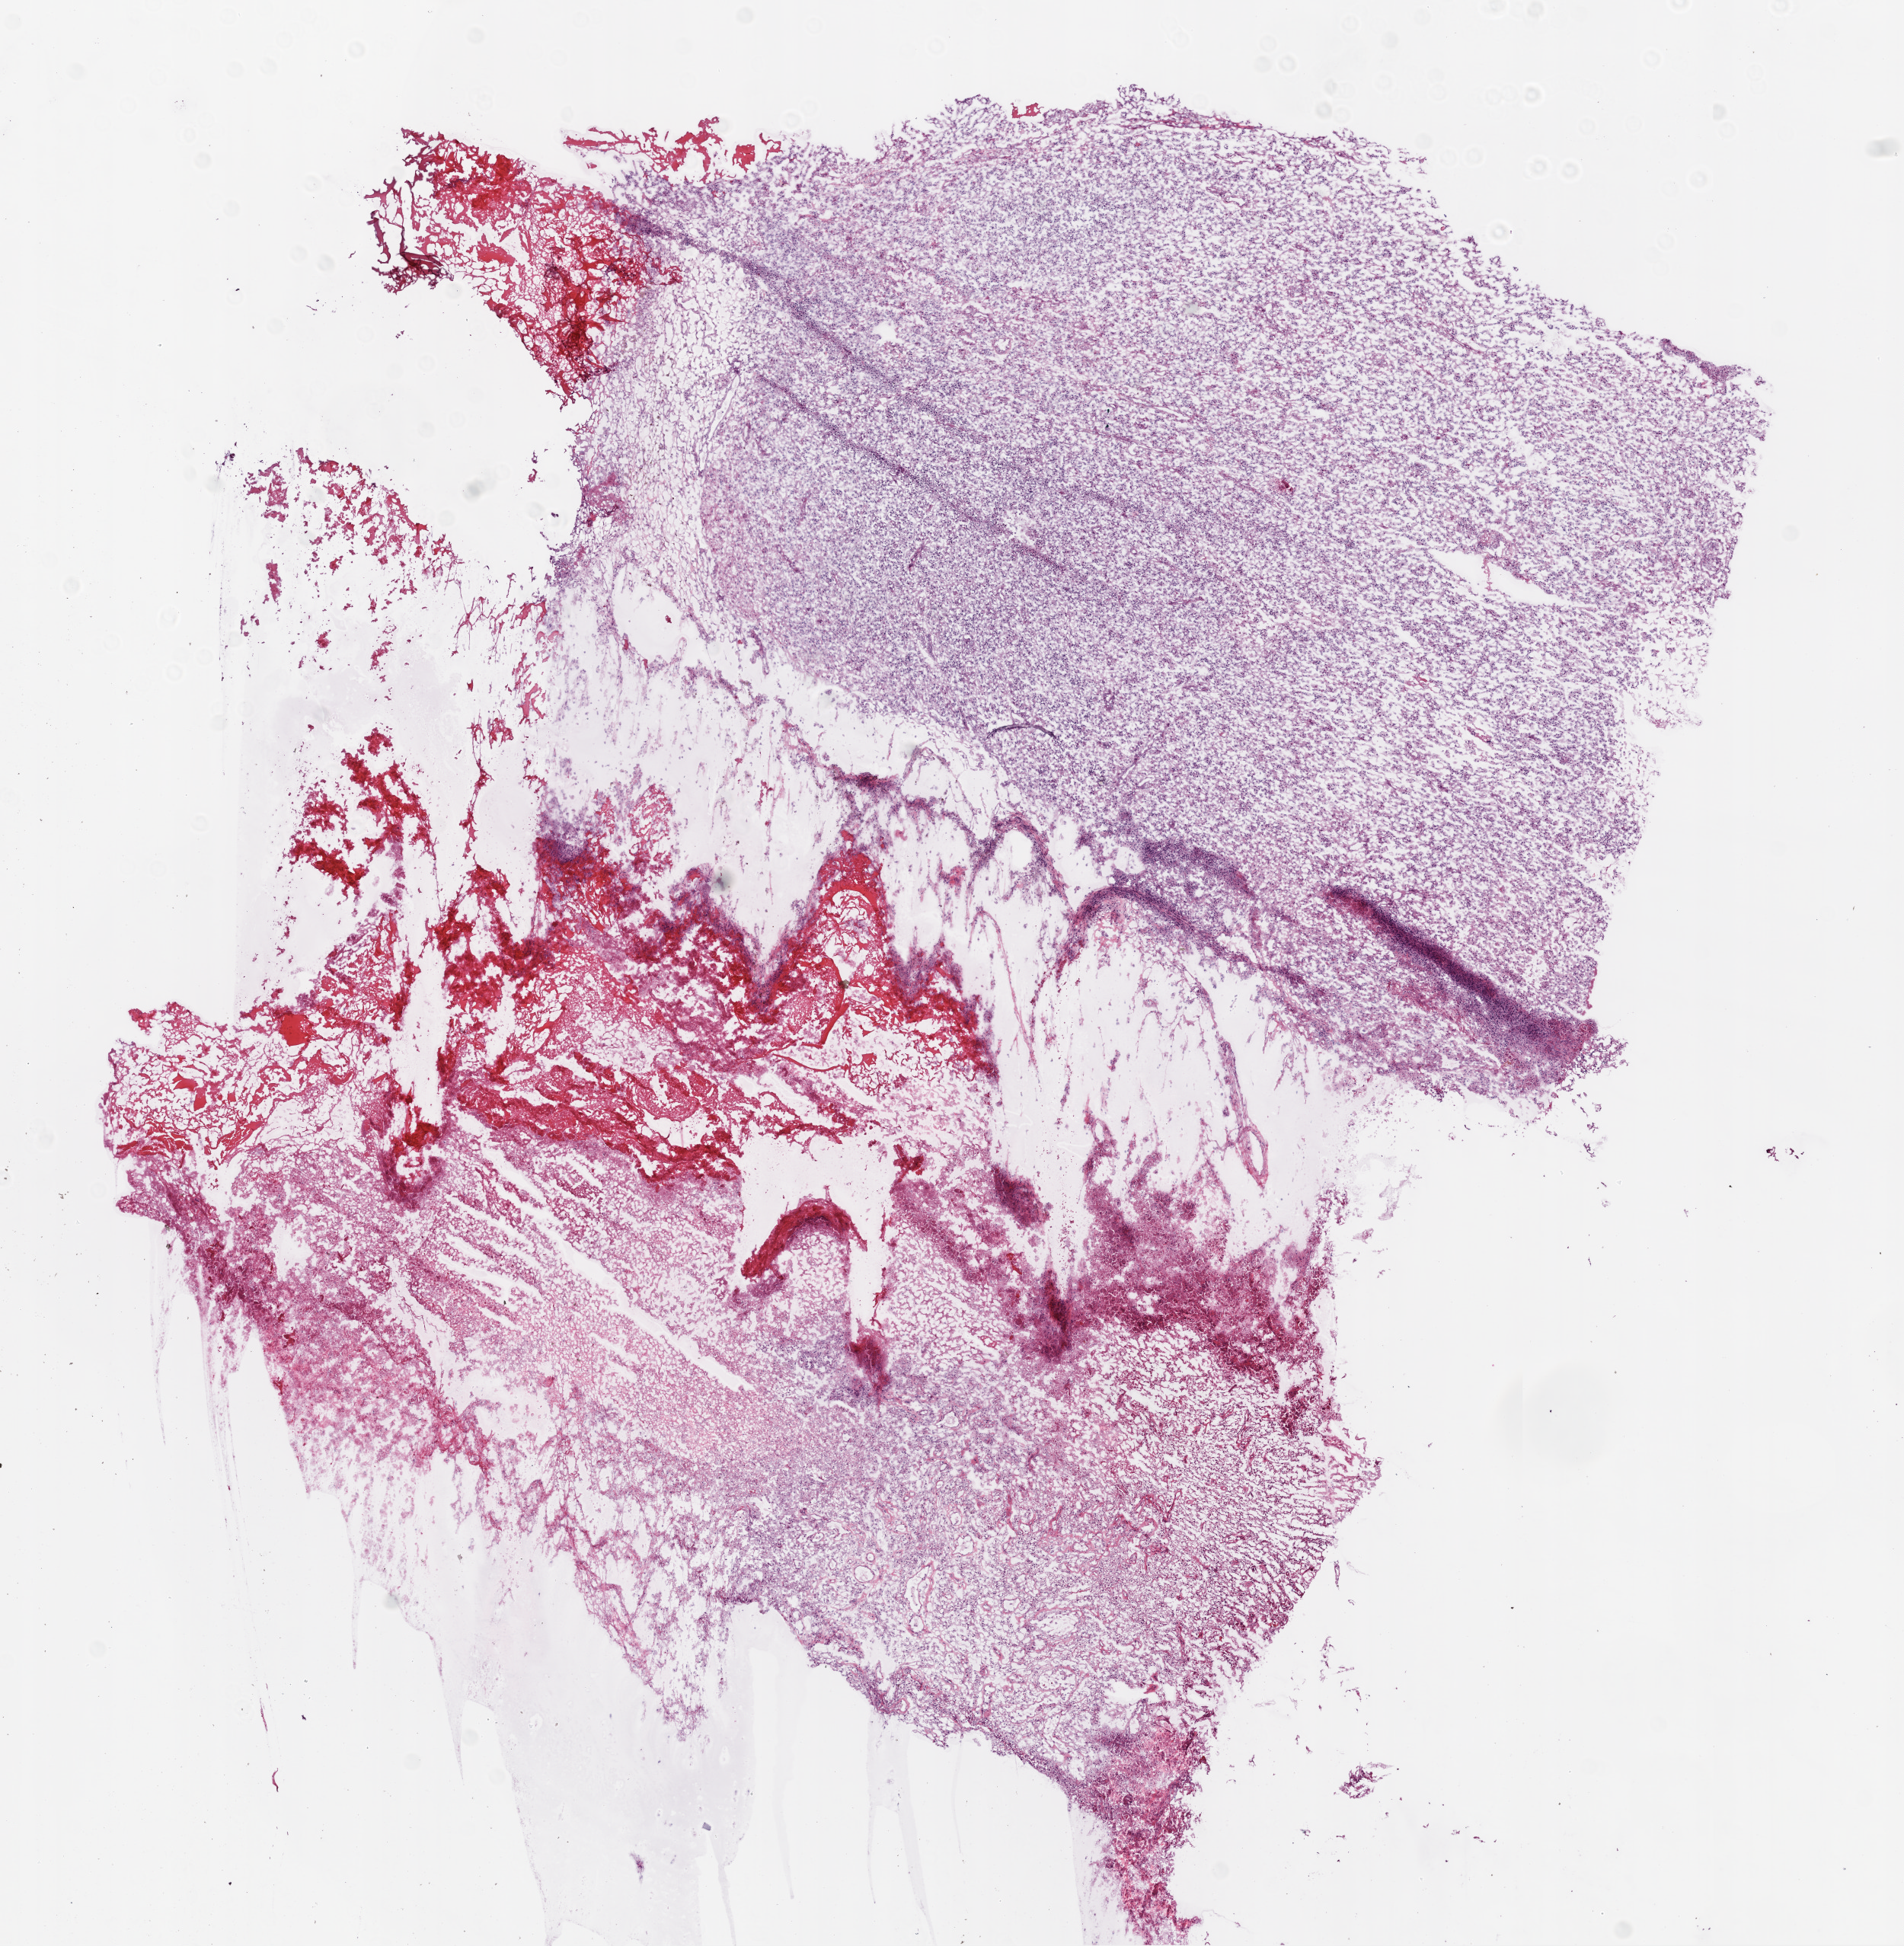
H&E-stained whole-slide image — low-resolution overview of the scanned area, about 10.0 x 10.3 mm (acquisition: 20x scan), frozen section from the bottom of the tissue portion, primary tumour sample from the brain. Patient: male, age at initial diagnosis 53 years. Composition of this section per pathologist review: tumour cells 65%, tumour nuclei 90%, normal cells 0%, stromal cells 10%, necrosis 25%.
Histologic diagnosis: Glioblastoma.